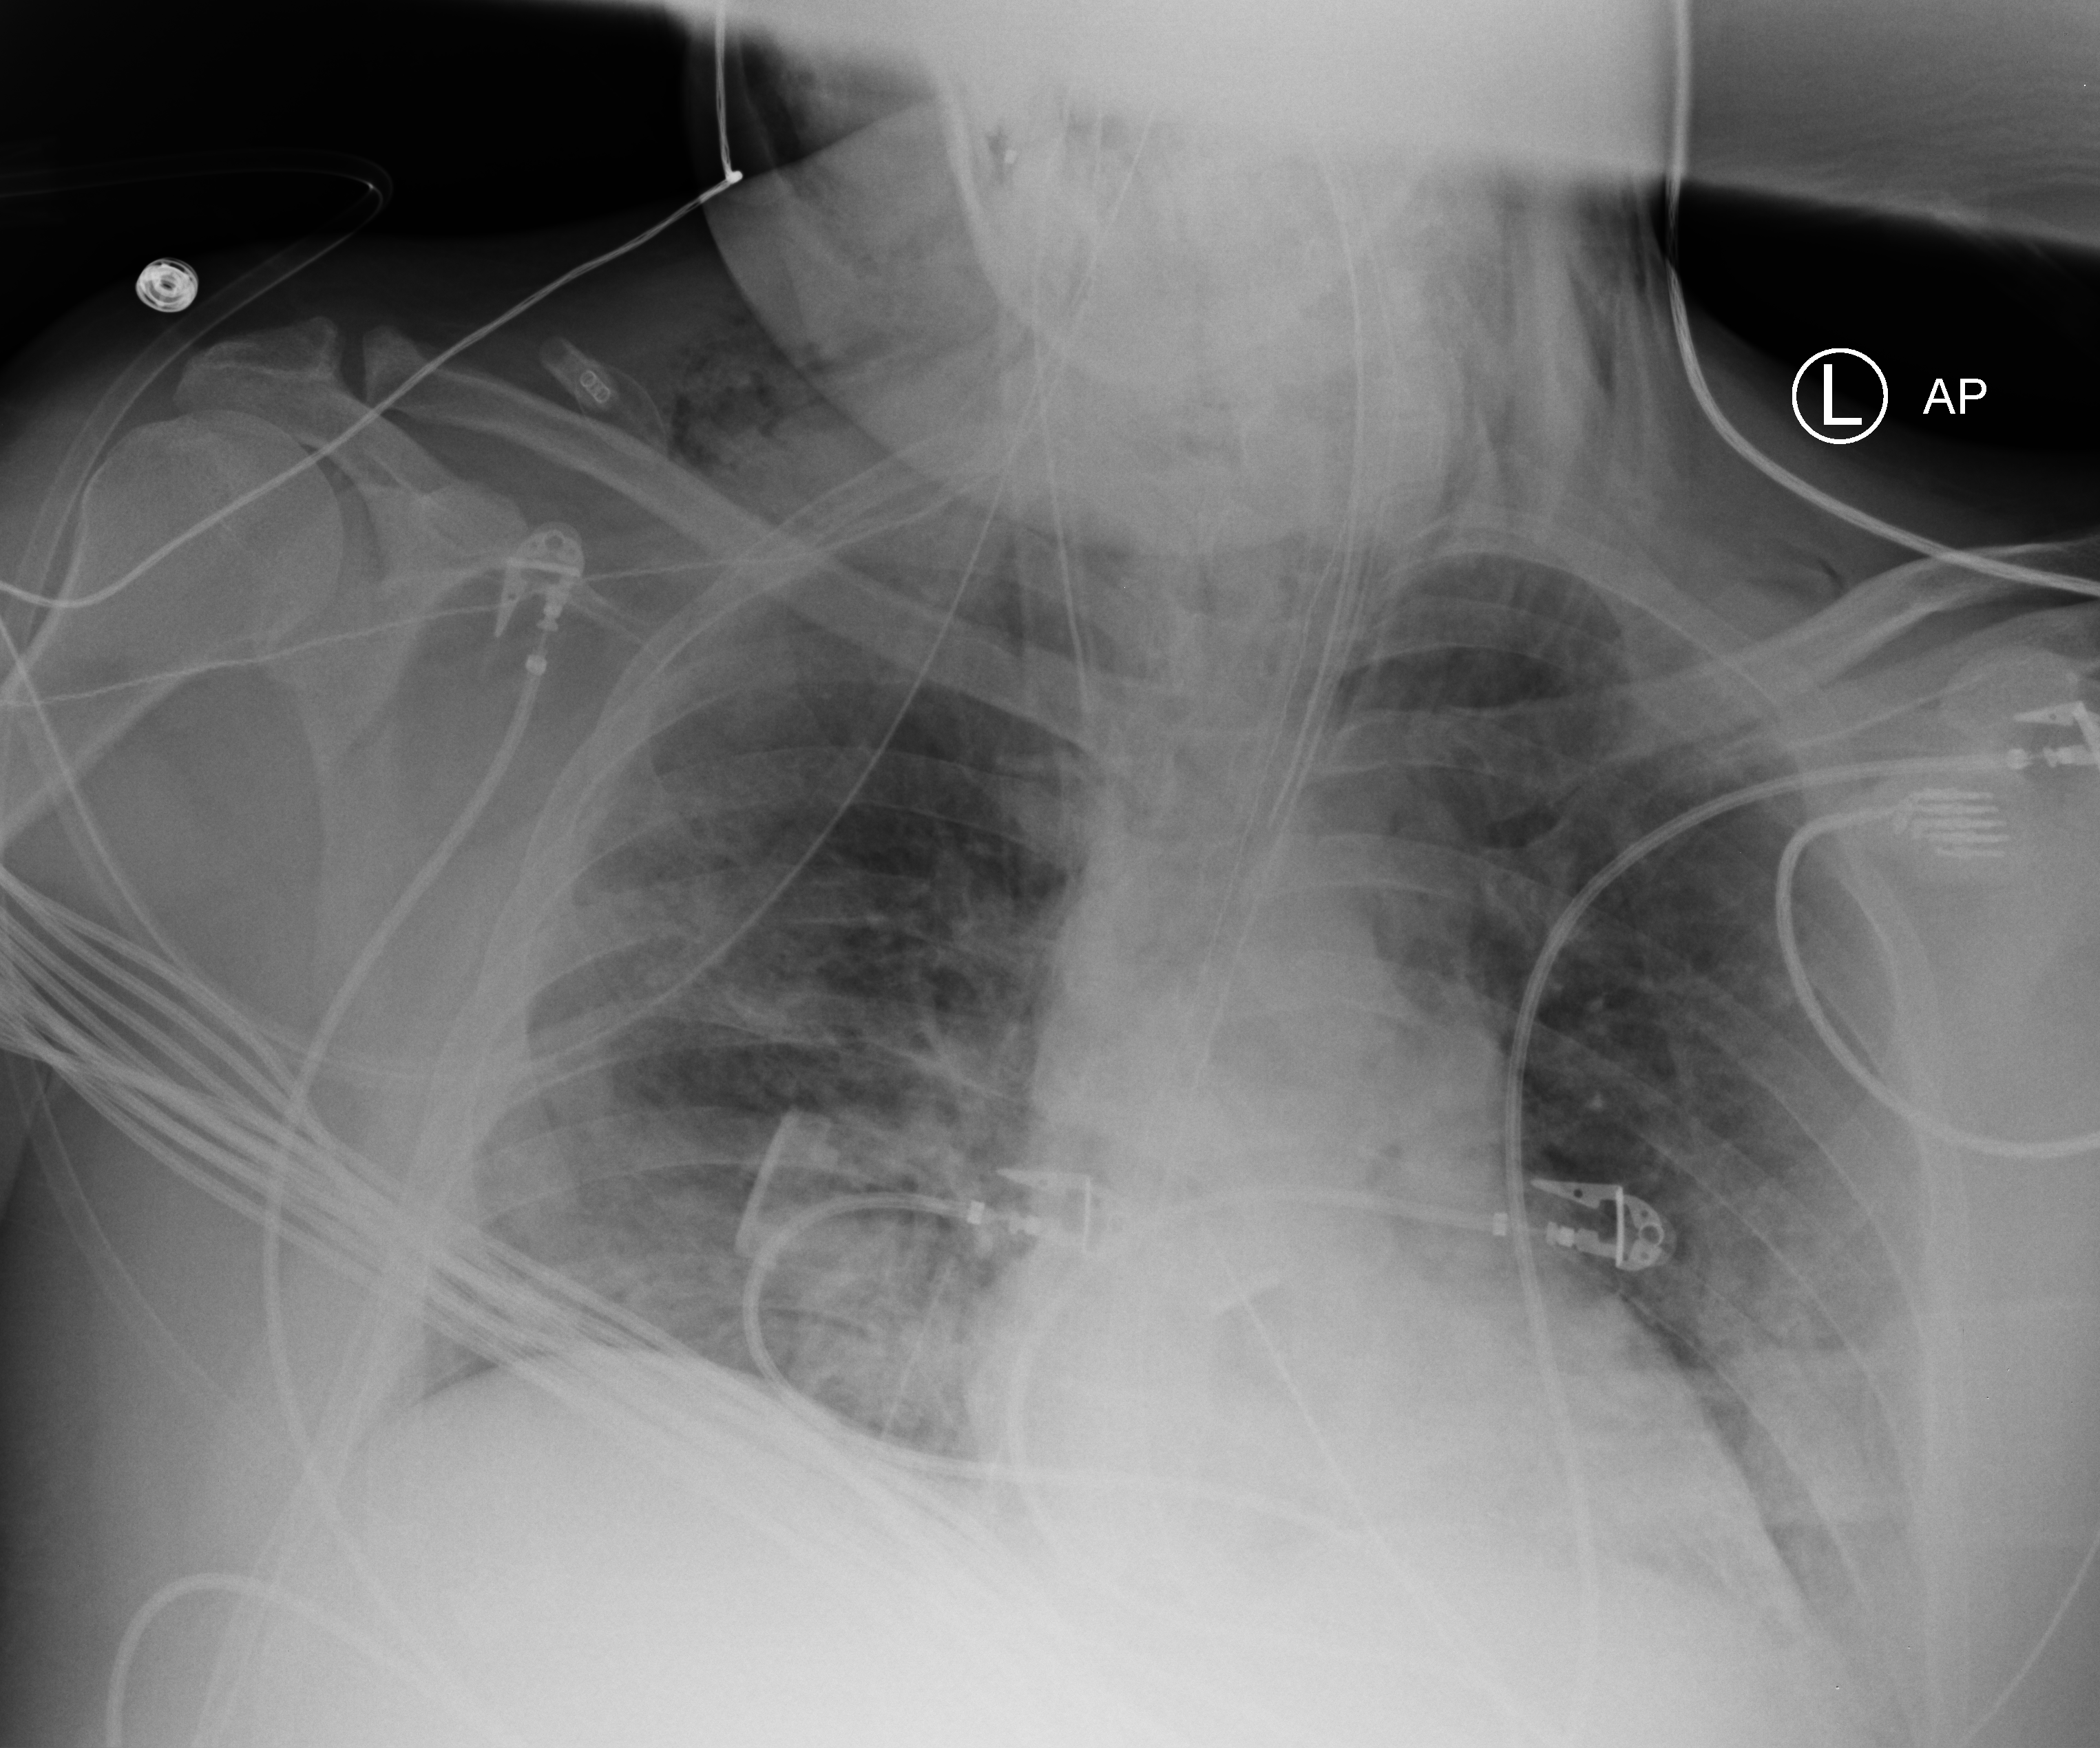
Portable chest radiograph, anteroposterior (AP) projection. Patient hospitalised with COVID-19, aged 18–59 years.
From the hospital-stay record, not from the radiograph (when in the stay this image was taken is not recorded):
- mechanically ventilated during this hospital stay: yes